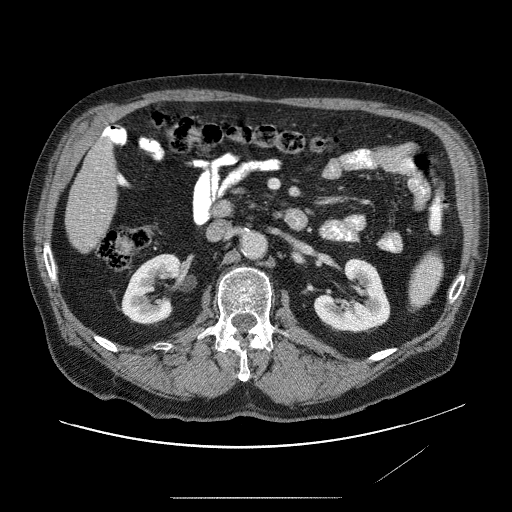
Contrast-enhanced abdominal CT (liver protocol), one axial slice; slice 14 of 89 in the series (ordered by position); reconstruction kernel STANDARD; 120 kVp; soft-tissue window (W 400 / L 40 HU); 2.5 mm slice thickness; 512 × 512 image matrix. From the clinical record (not read from this slice): diagnosis: hepatocellular carcinoma (patient treated with transarterial chemoembolisation; whether this scan precedes or follows treatment is not stated here); TNM stage (as recorded): Stage-IVA; Child-Pugh class: A.
Outlined on this slice (semi-automatic segmentation, software-assisted and operator-edited):
- liver parenchyma outside the tumour (the mass and vessels are separate outlines, so this box may not span the whole liver): bounding box (x1, y1, x2, y2) in pixels: (64, 130, 126, 256)
- liver vessels: (97, 170, 111, 217)